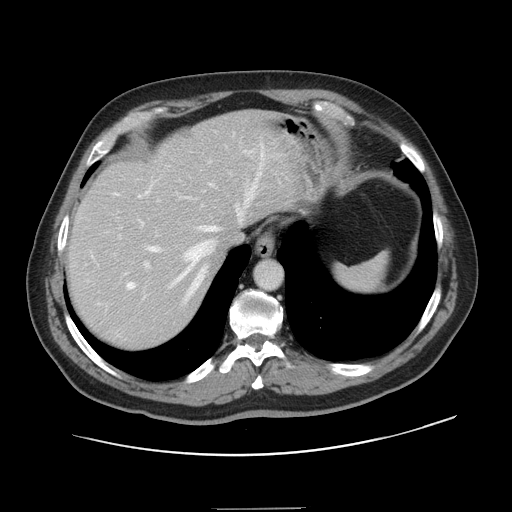
Contrast-enhanced abdominal CT, one axial slice; position 116 of 143 along the scan axis; intravenous contrast given; soft-tissue window (W 400 / L 40 HU); 2.5 mm slice thickness; 512 × 512 image matrix, field of view 402 × 402 mm. Male patient, age 62 years. Case-level facts recorded for this patient, not image findings: diagnosis: colorectal cancer liver metastases, imaged before liver resection; multiple liver metastases: yes; largest metastasis: 2.7 cm; disease in both lobes: no.
Structures marked on this image (outlined manually by an expert reader):
- hepatic veins: bounding box (x1, y1, x2, y2) in pixels: (115, 150, 264, 294)
- liver: (69, 113, 301, 349)
- planned liver remnant (the part of the liver to remain after resection): (69, 113, 301, 285)
- portal vein (with intrahepatic branches): (119, 148, 264, 269)